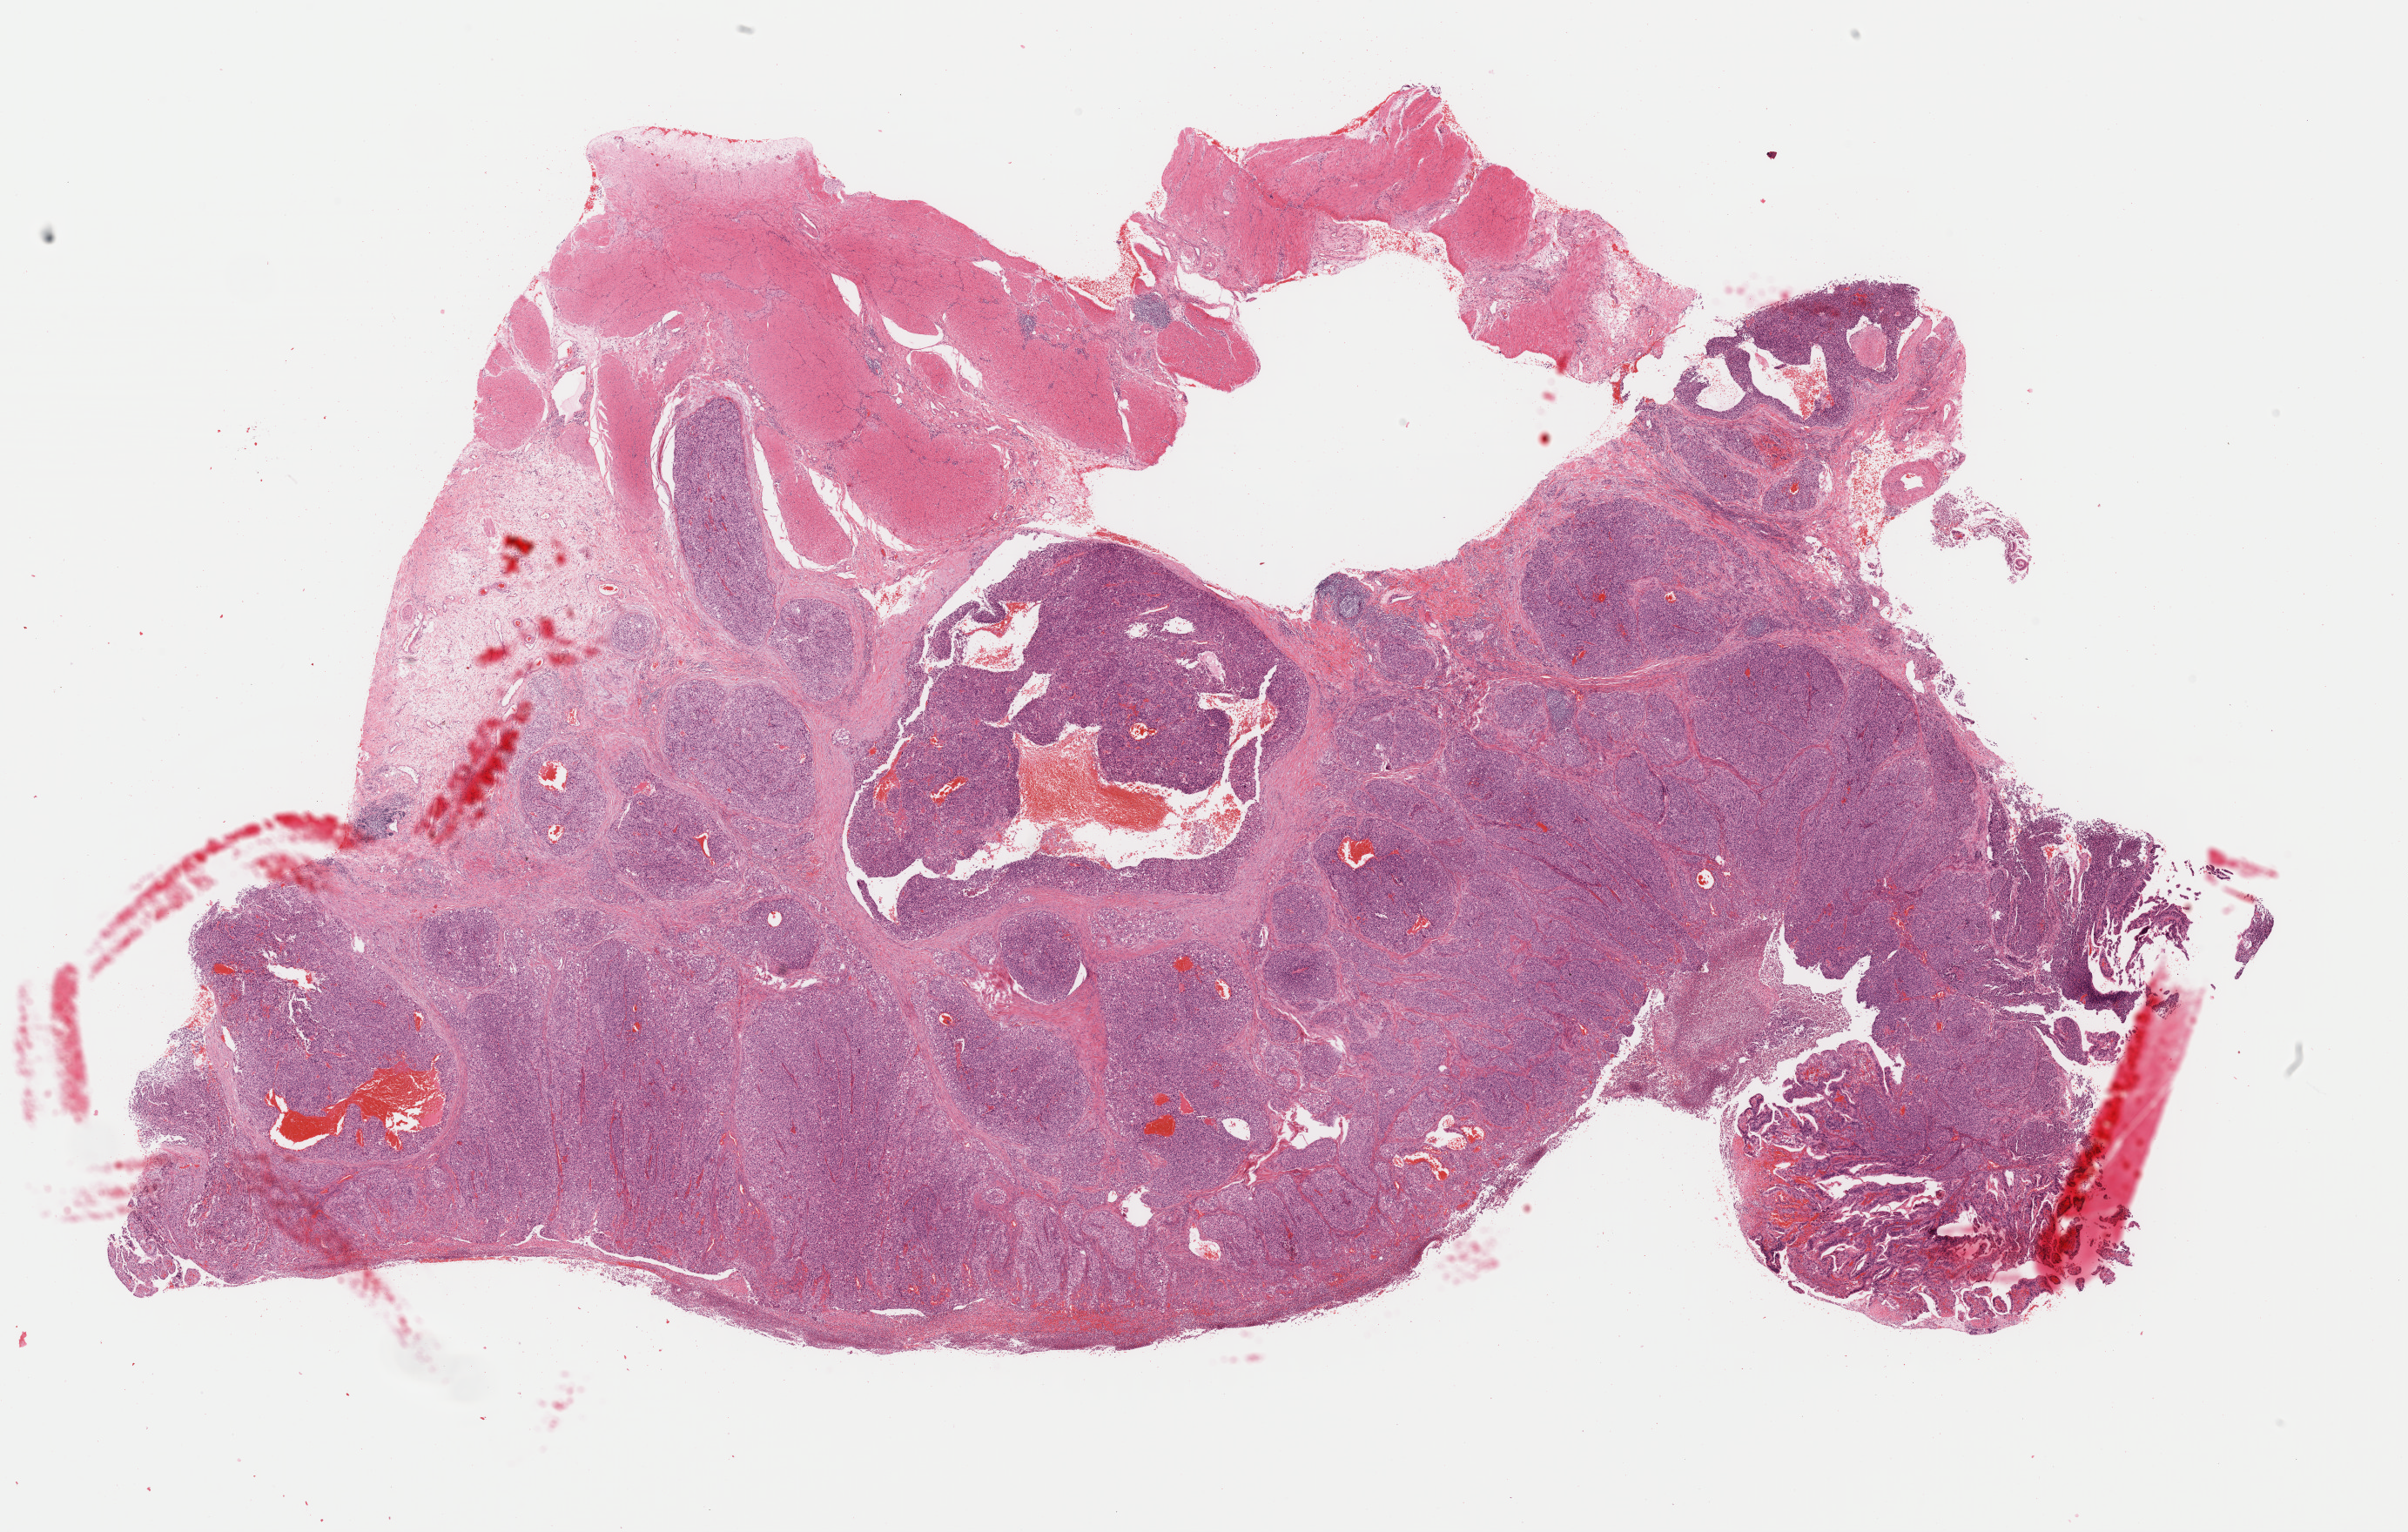
Whole-slide histology image, H&E — shown as a low-resolution overview of the whole scanned area (about 21.9 x 13.9 mm, acquisition: 40x scan), formalin-fixed paraffin-embedded (FFPE) diagnostic section, sample: primary tumour, stomach. Male, age 77 years at initial diagnosis. Histologic grade: G3 (poorly differentiated).
AJCC pathologic stage: IIIC (7th edition). Lymph nodes positive (case pathology): 7 of 15 examined. Diagnosis: Adenocarcinoma, NOS (fundus of stomach).